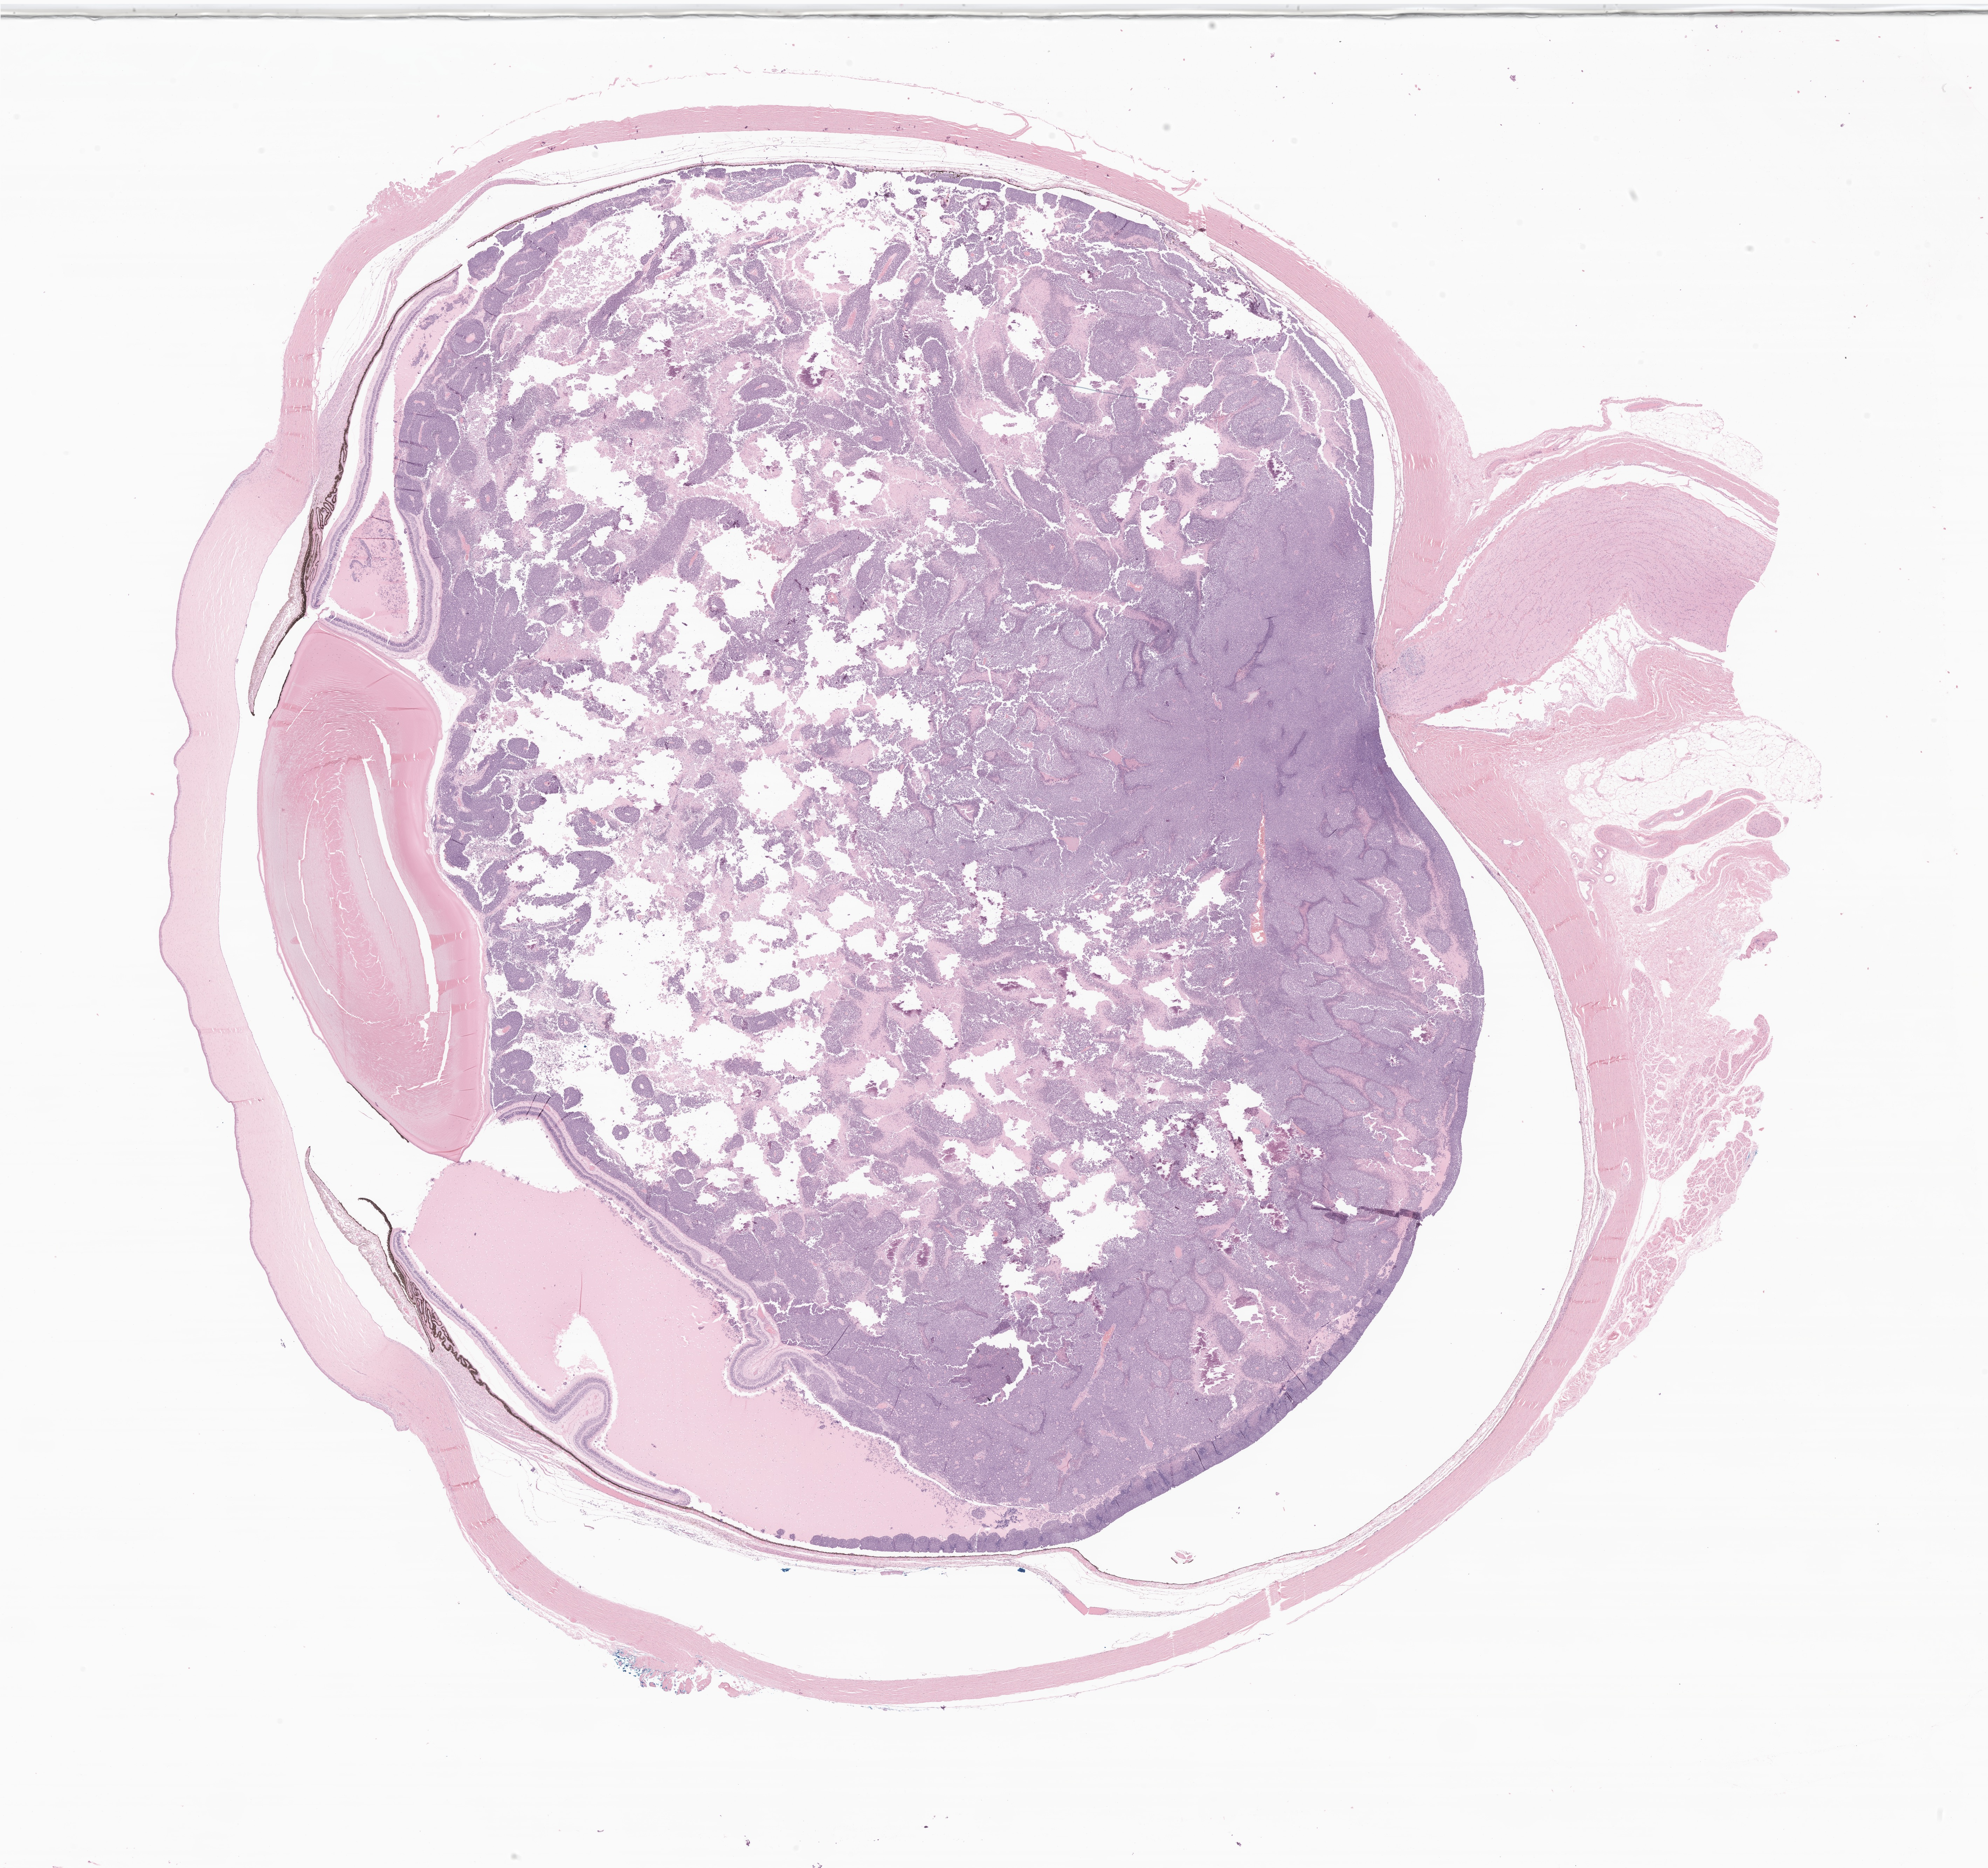
Digitized H&E-stained section of tumor tissue from the eye, low-resolution overview of the scanned area, about 23.9 x 22.5 mm. FFPE section. Patient female; age 362 days.
Diagnosis (ICD-O-3 morphology term): Retinoblastoma, NOS.